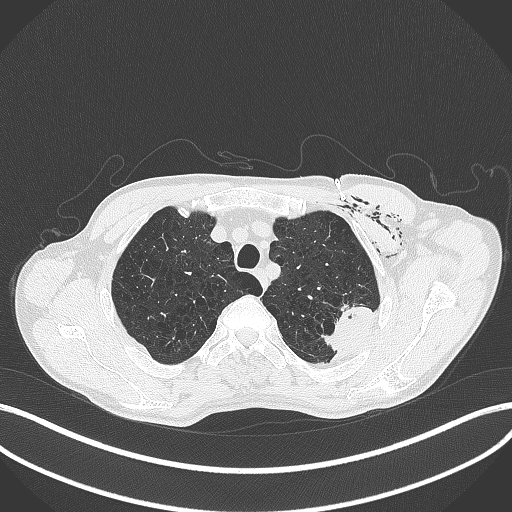
Chest CT, one axial slice; position 344 of 457 along the scan axis; lung window (W 1500 / L -600 HU); 512 × 512 image matrix, field of view 400 × 400 mm. Patient: male, 58 years. From the clinical record (not read from this slice): clinical TNM (as recorded): T3 N0 M0.
Structures marked on this image (rectangle marked by the reading radiologist):
- lung tumour (recorded histology: adenocarcinoma): bounding box (x1, y1, x2, y2) in pixels: (323, 300, 377, 361)